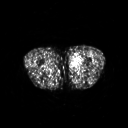
FDG PET of an extremity soft-tissue mass (from a PET/CT study), one axial slice. 3.27 mm slice thickness. 128 × 128 image matrix. Patient: male, 29 years. From the clinical record (not read from this slice): histological type: mixoid liposarcoma; grade: low; site of the primary tumour: left thigh.
Annotated regions visible in this slice (expert contour drawn on MRI and transferred to this co-registered scan by the dataset authors):
- gross tumour volume (mass): bounding box [x1, y1, x2, y2] px = [70, 53, 82, 70]